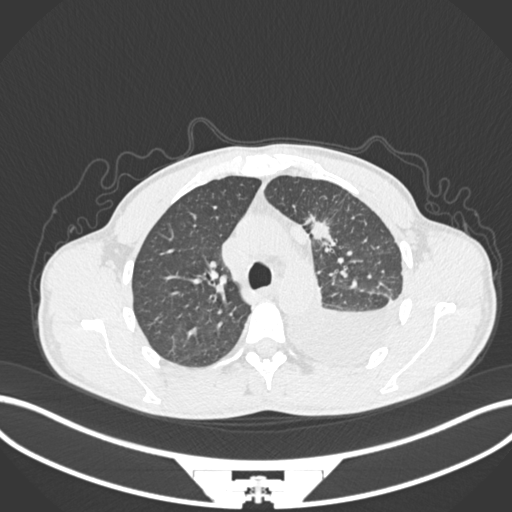
Chest CT, one axial slice. Position 153 of 244 along the scan axis. Reconstruction kernel B30f. Lung window (W 1500 / L -600 HU). 1 mm slice thickness. 512 × 512 image matrix, field of view 400 × 400 mm. Male patient, age 49 years. Case-level facts recorded for this patient, not image findings: clinical TNM (as recorded): T1c N1 M1.
Outlined on this slice (rectangle marked by the reading radiologist):
- lung tumour (recorded histology: adenocarcinoma): bounding box <308,210,336,246> (left, top, right, bottom; pixels)